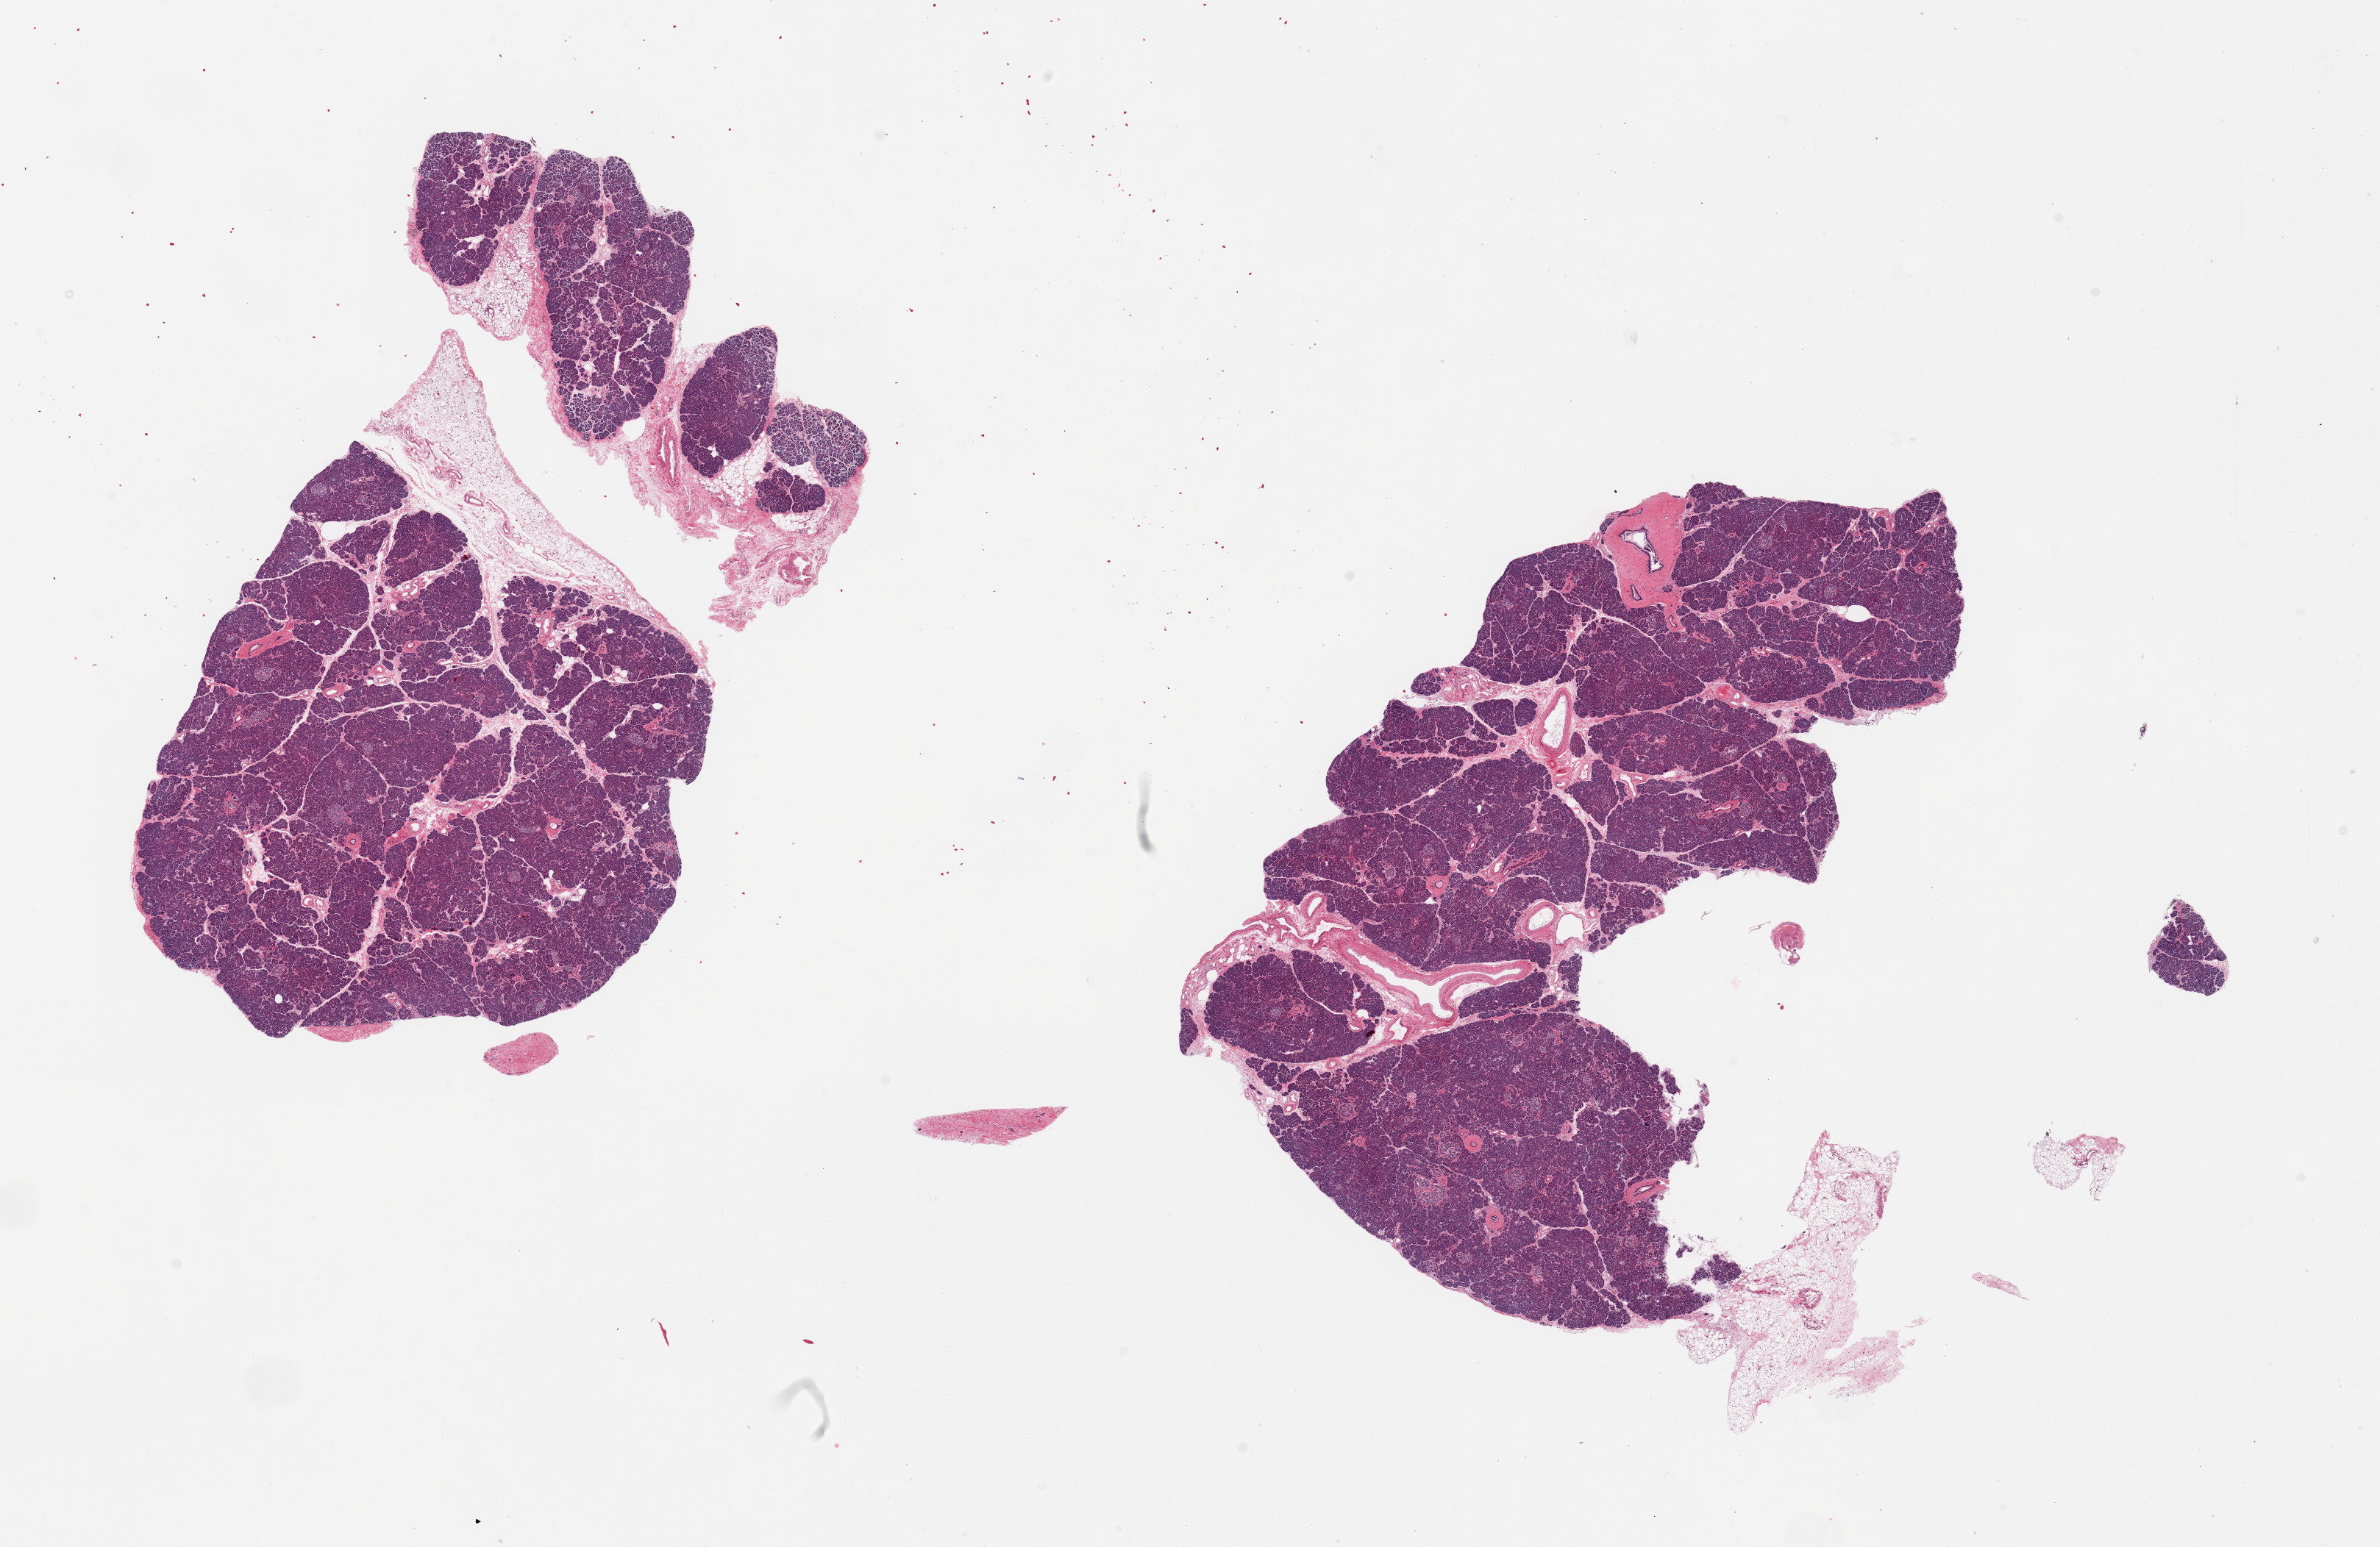
Digitized H&E-stained section — shown as a low-resolution overview of the whole scanned area (about 25.6 x 16.6 mm, from a 20x scan), PAXgene-fixed paraffin-embedded (PFPE) section, target tissue: pancreas, donor tissue sample.
Reviewer comment on this tissue sample: 2 pieces, 10-20% adherent fat; Islets well-preserved.